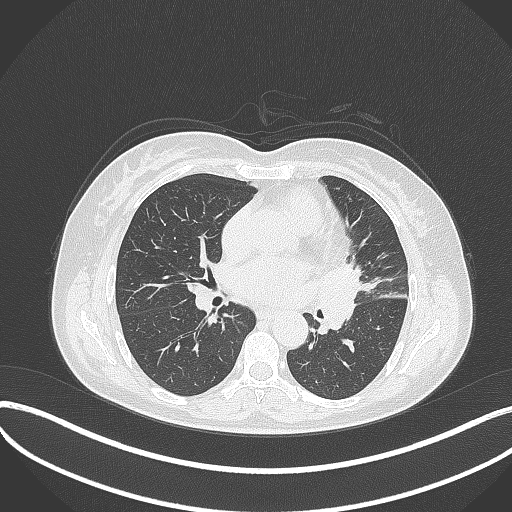
Chest CT, one axial slice. Slice 179 of 373 in the series (ordered by position). Reconstruction kernel B70f. 120 kVp. Lung window (W 1500 / L -600 HU). 512 × 512 image matrix, field of view 400 × 400 mm. Patient: female, 54 years. Case-level facts recorded for this patient, not image findings: clinical TNM (as recorded): T2a N1 M0; histopathological grade: G3.
Structures marked on this image (bounding box drawn by a radiologist):
- lung tumour (recorded histology: small cell carcinoma): bounding box <318,256,367,332> (left, top, right, bottom; pixels)